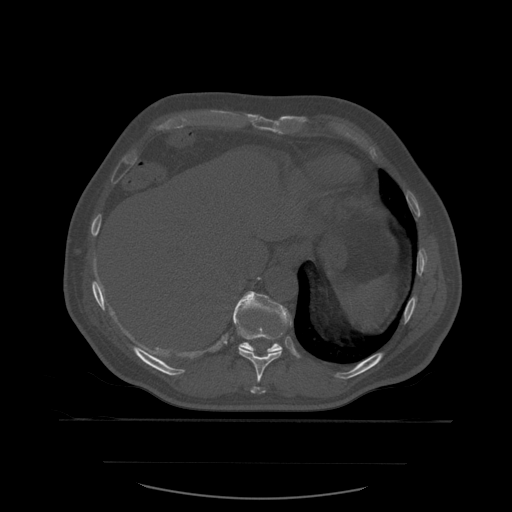
CT including the spine, one axial slice; slice 311 of 590 in the series (ordered by position); bone window (W 1800 / L 400 HU); 1.25 mm slice thickness; 512 × 512 image matrix, field of view 479 × 479 mm. Patient age 71 years. Case-level facts recorded for this patient, not image findings: primary cancer: lung.
Outlined on this slice (semi-automatically segmented with operator editing):
- T10 vertebra: bounding box <233,293,292,394> (left, top, right, bottom; pixels)
- T11 vertebra: <233,291,293,353>
- T9 vertebra: <251,388,254,394>